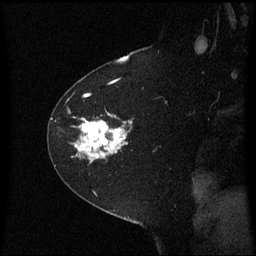
Breast MRI (dynamic contrast-enhanced), one sagittal slice. Slice 46 of 60 in the series (ordered by position). Dynamic contrast-enhanced series, image 2 of 3 at this slice position (ordered by acquisition). 1.5 T. TE 4.2 ms, TR 8.4 ms. 2 mm slice thickness. 256 × 256 image matrix. Patient: female, 60 years. From the clinical record (not read from this slice): setting: breast cancer imaged before/during neoadjuvant chemotherapy; receptor status: triple-negative.
Outlined on this slice (semi-automatically segmented with operator editing):
- analysis volume of interest (the breast-tissue region the enhancement analysis was run in; not a lesion): bounding box (x1, y1, x2, y2) in pixels: (49, 99, 136, 181)
- tumour enhancement mask (voxels above the 70 % enhancement threshold inside the analysis volume of interest): (77, 121, 128, 159)